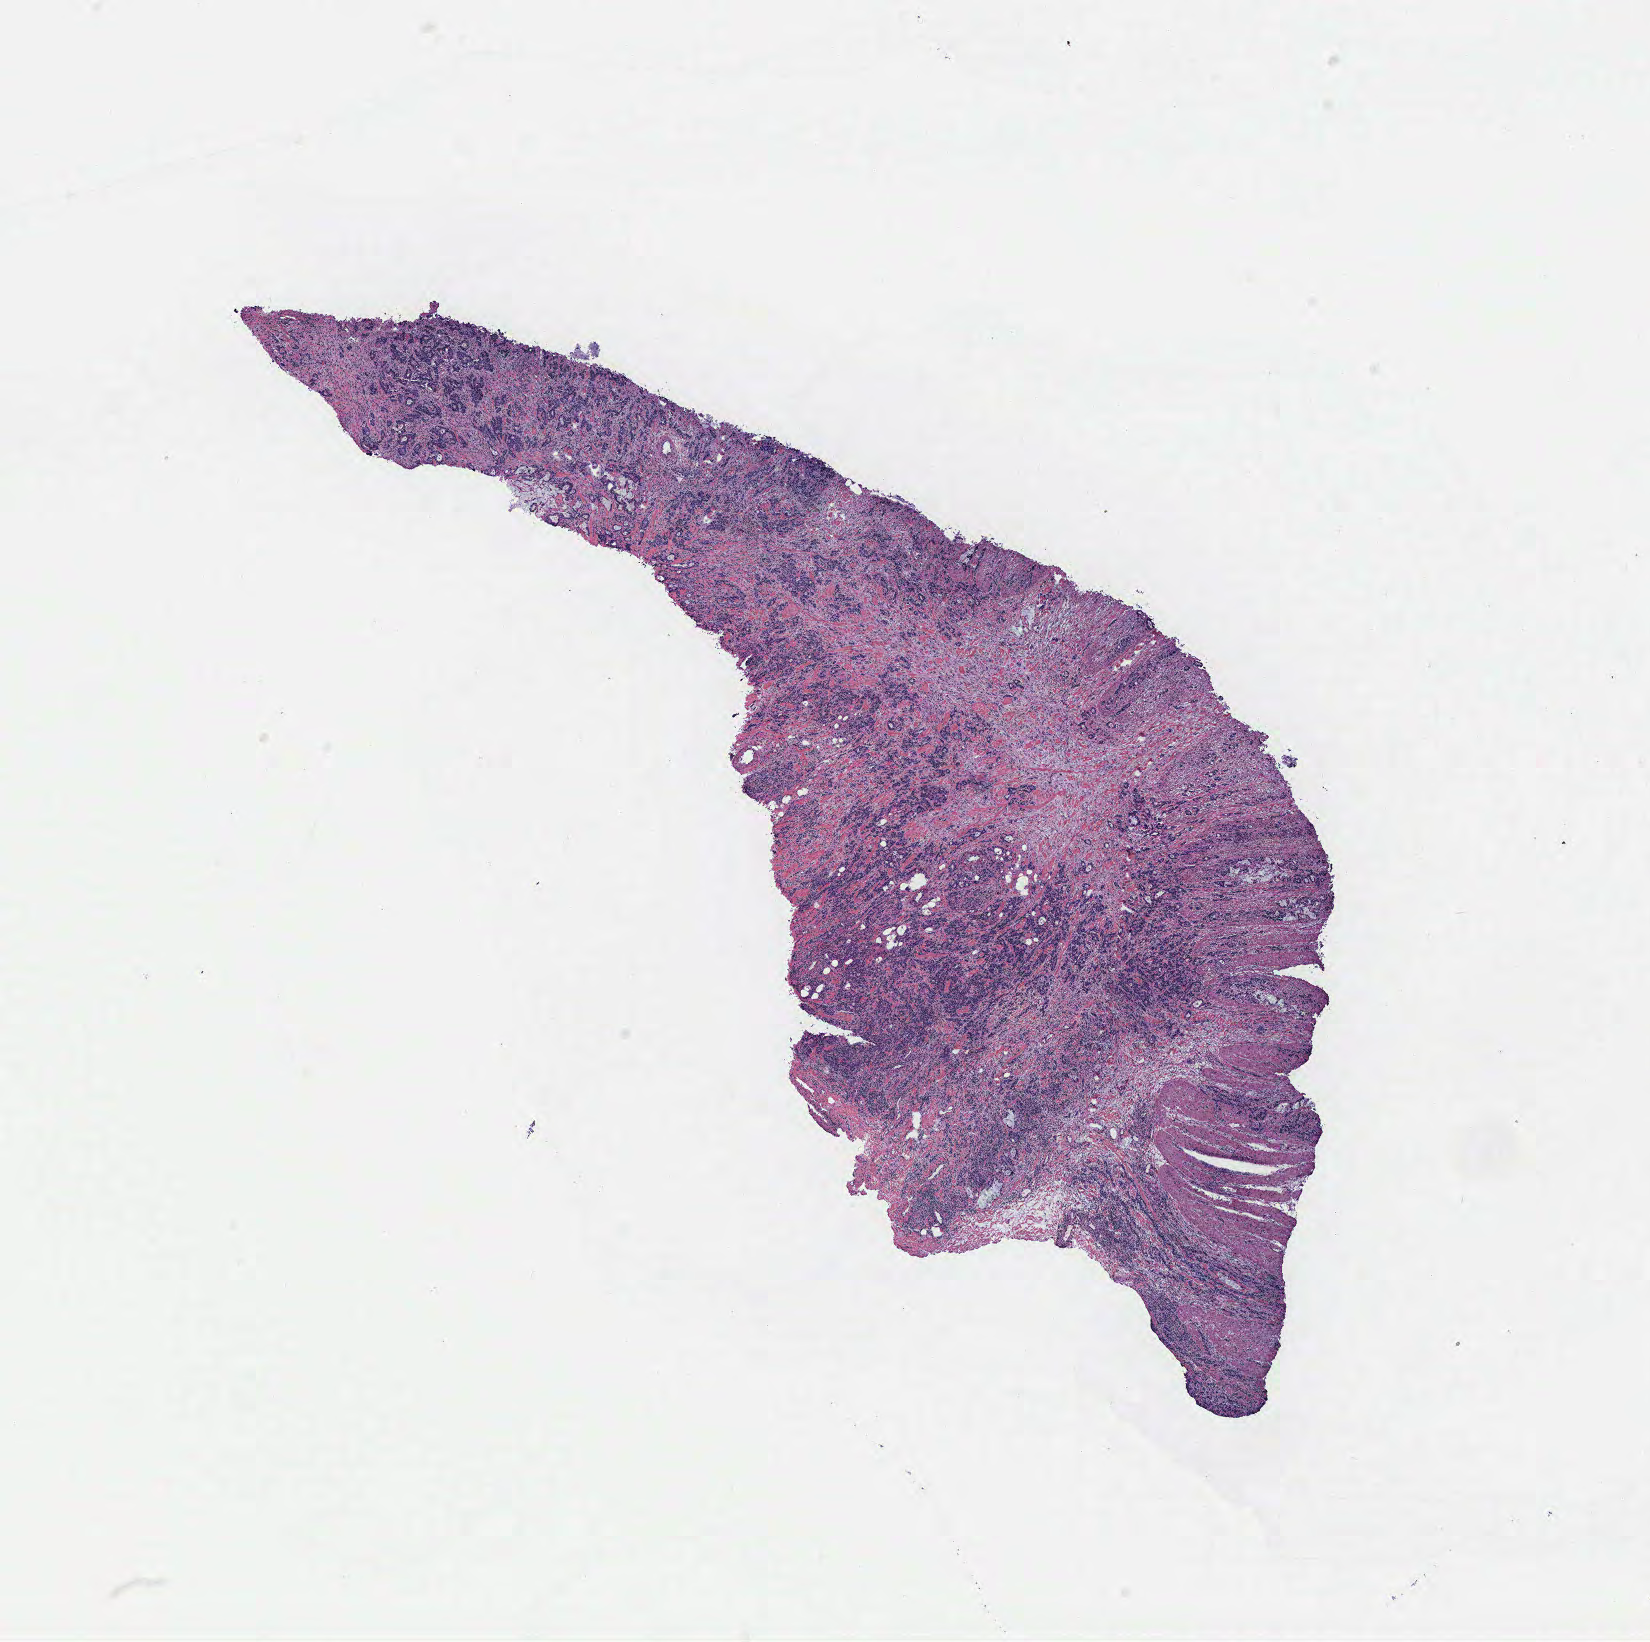
Whole-slide histology image, H&E, a low-resolution overview of the entire scanned area, about 13.2 x 13.1 mm (acquisition: 40x scan). Colon, tissue type not recorded. Female patient.
Patient diagnosis: Adenocarcinoma, NOS.